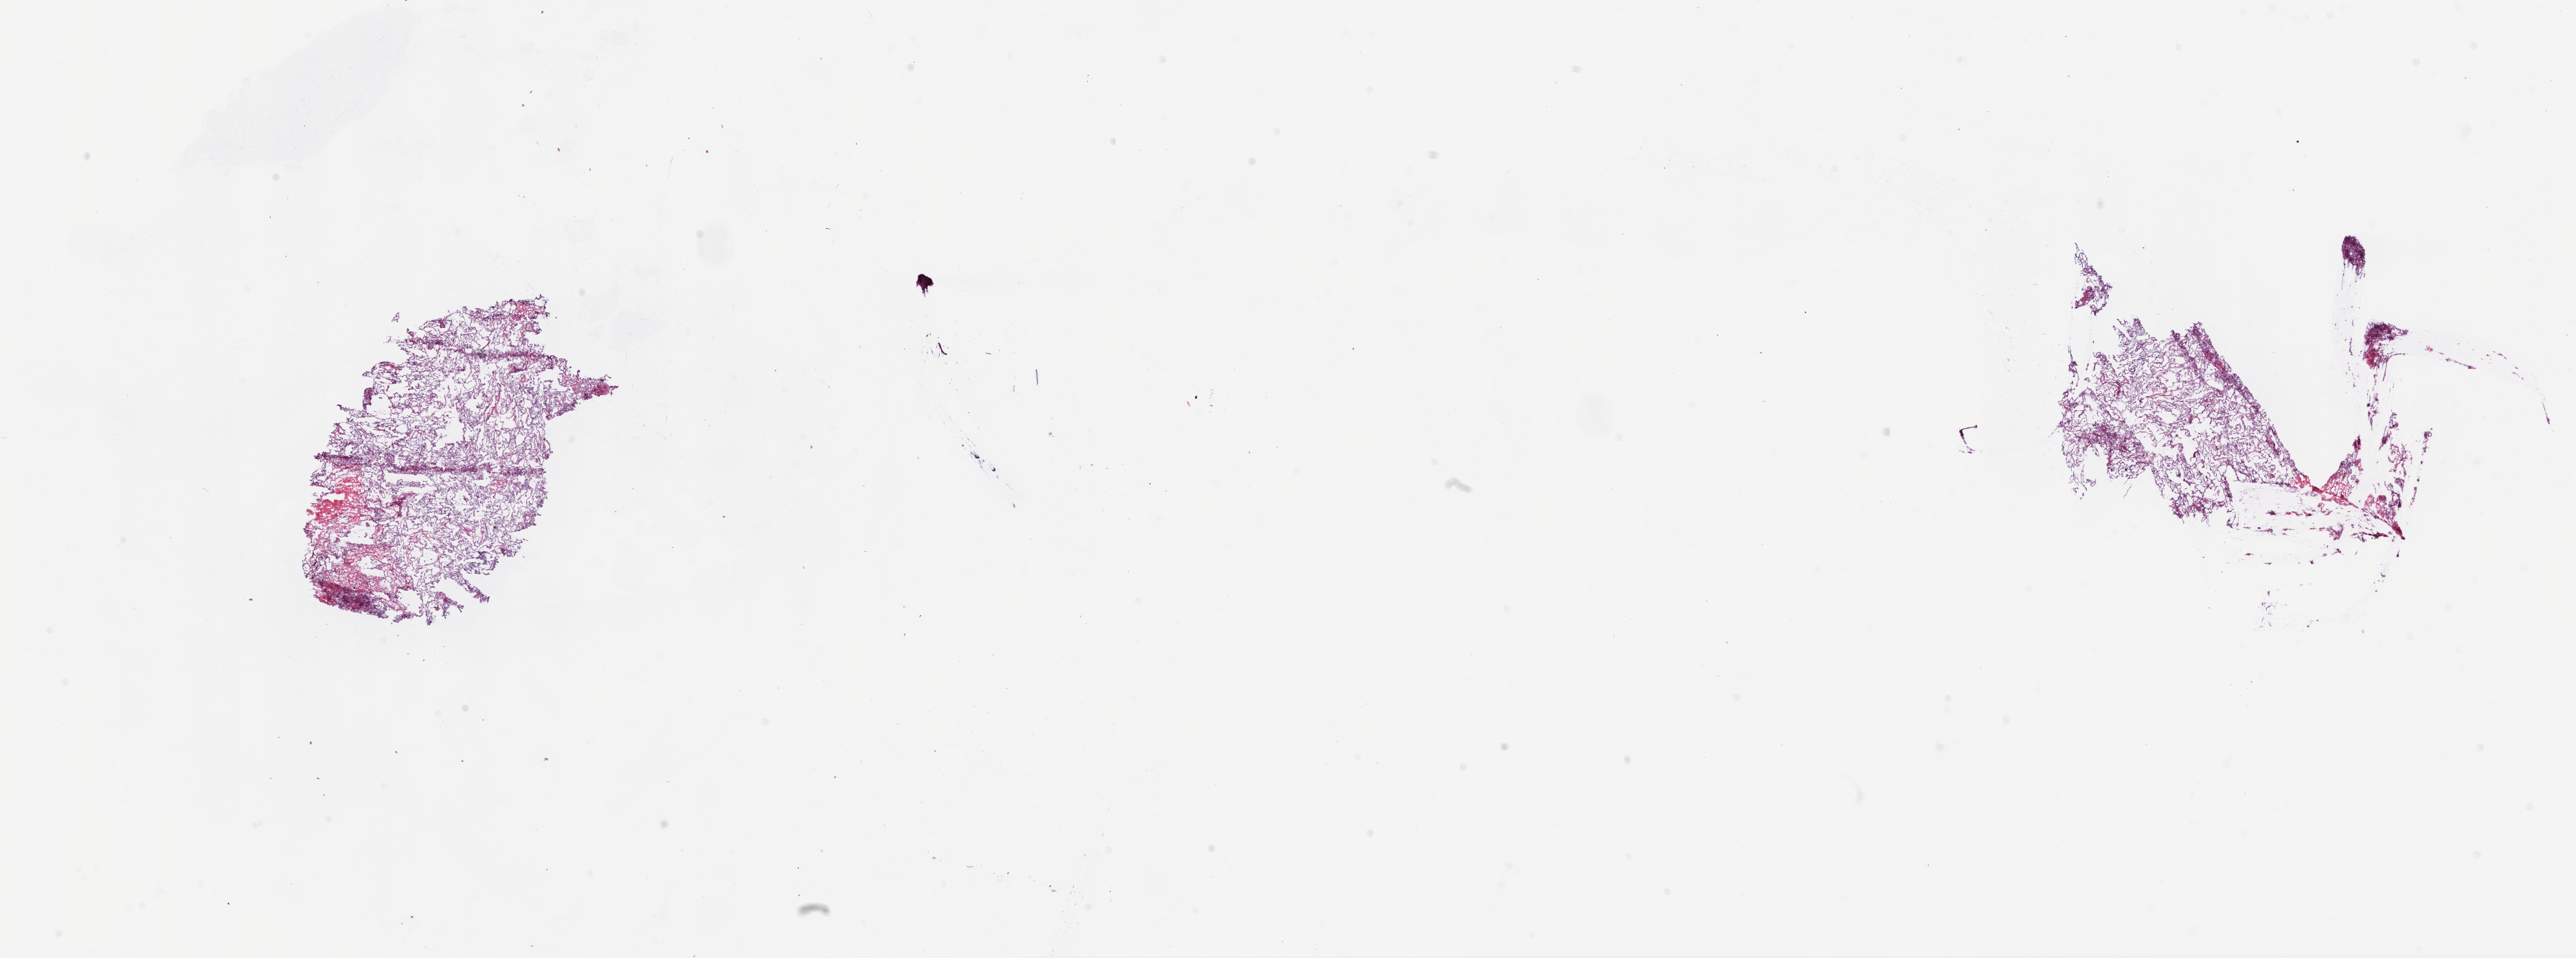
Whole-slide histology image, Hematoxylin and eosin (H&E) stained — shown as a low-resolution overview of the whole scanned area (about 30.1 x 11.2 mm). Frozen section from the top of the tissue portion. Lung, solid tissue normal (non-tumour tissue) sample. Male, age 74 years at initial diagnosis.
- this section: solid tissue normal sample (biorepository sample class)
- patient diagnosis: Basaloid squamous cell carcinoma (upper lobe, lung)